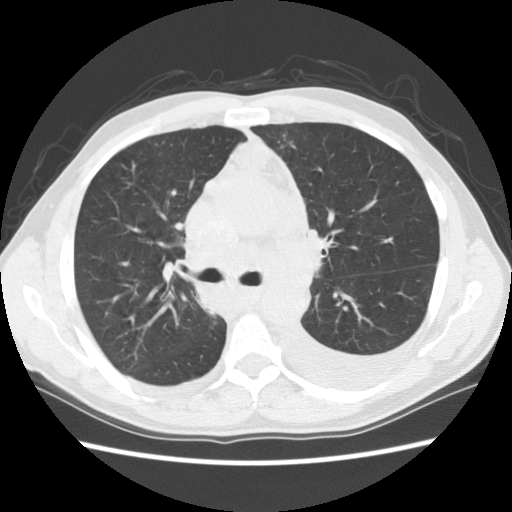
Low-dose screening chest CT, axial slice, first (baseline) screen, lung window (W 1500 / L -600 HU), standard (soft-tissue) reconstruction kernel (STANDARD), slice 42 of 135 in the series, 512 × 512 image matrix, field of view 346 × 346 mm. Male participant, aged 60 years at enrolment. Current smoker at enrolment.
Expert reader's lesion annotation, box from (x=178, y=236) to (x=291, y=325) px. Screening reader's record for this exam: no non-calcified nodule ≥4 mm recorded. Official screen result: negative screen, significant abnormalities not suspicious for lung cancer.